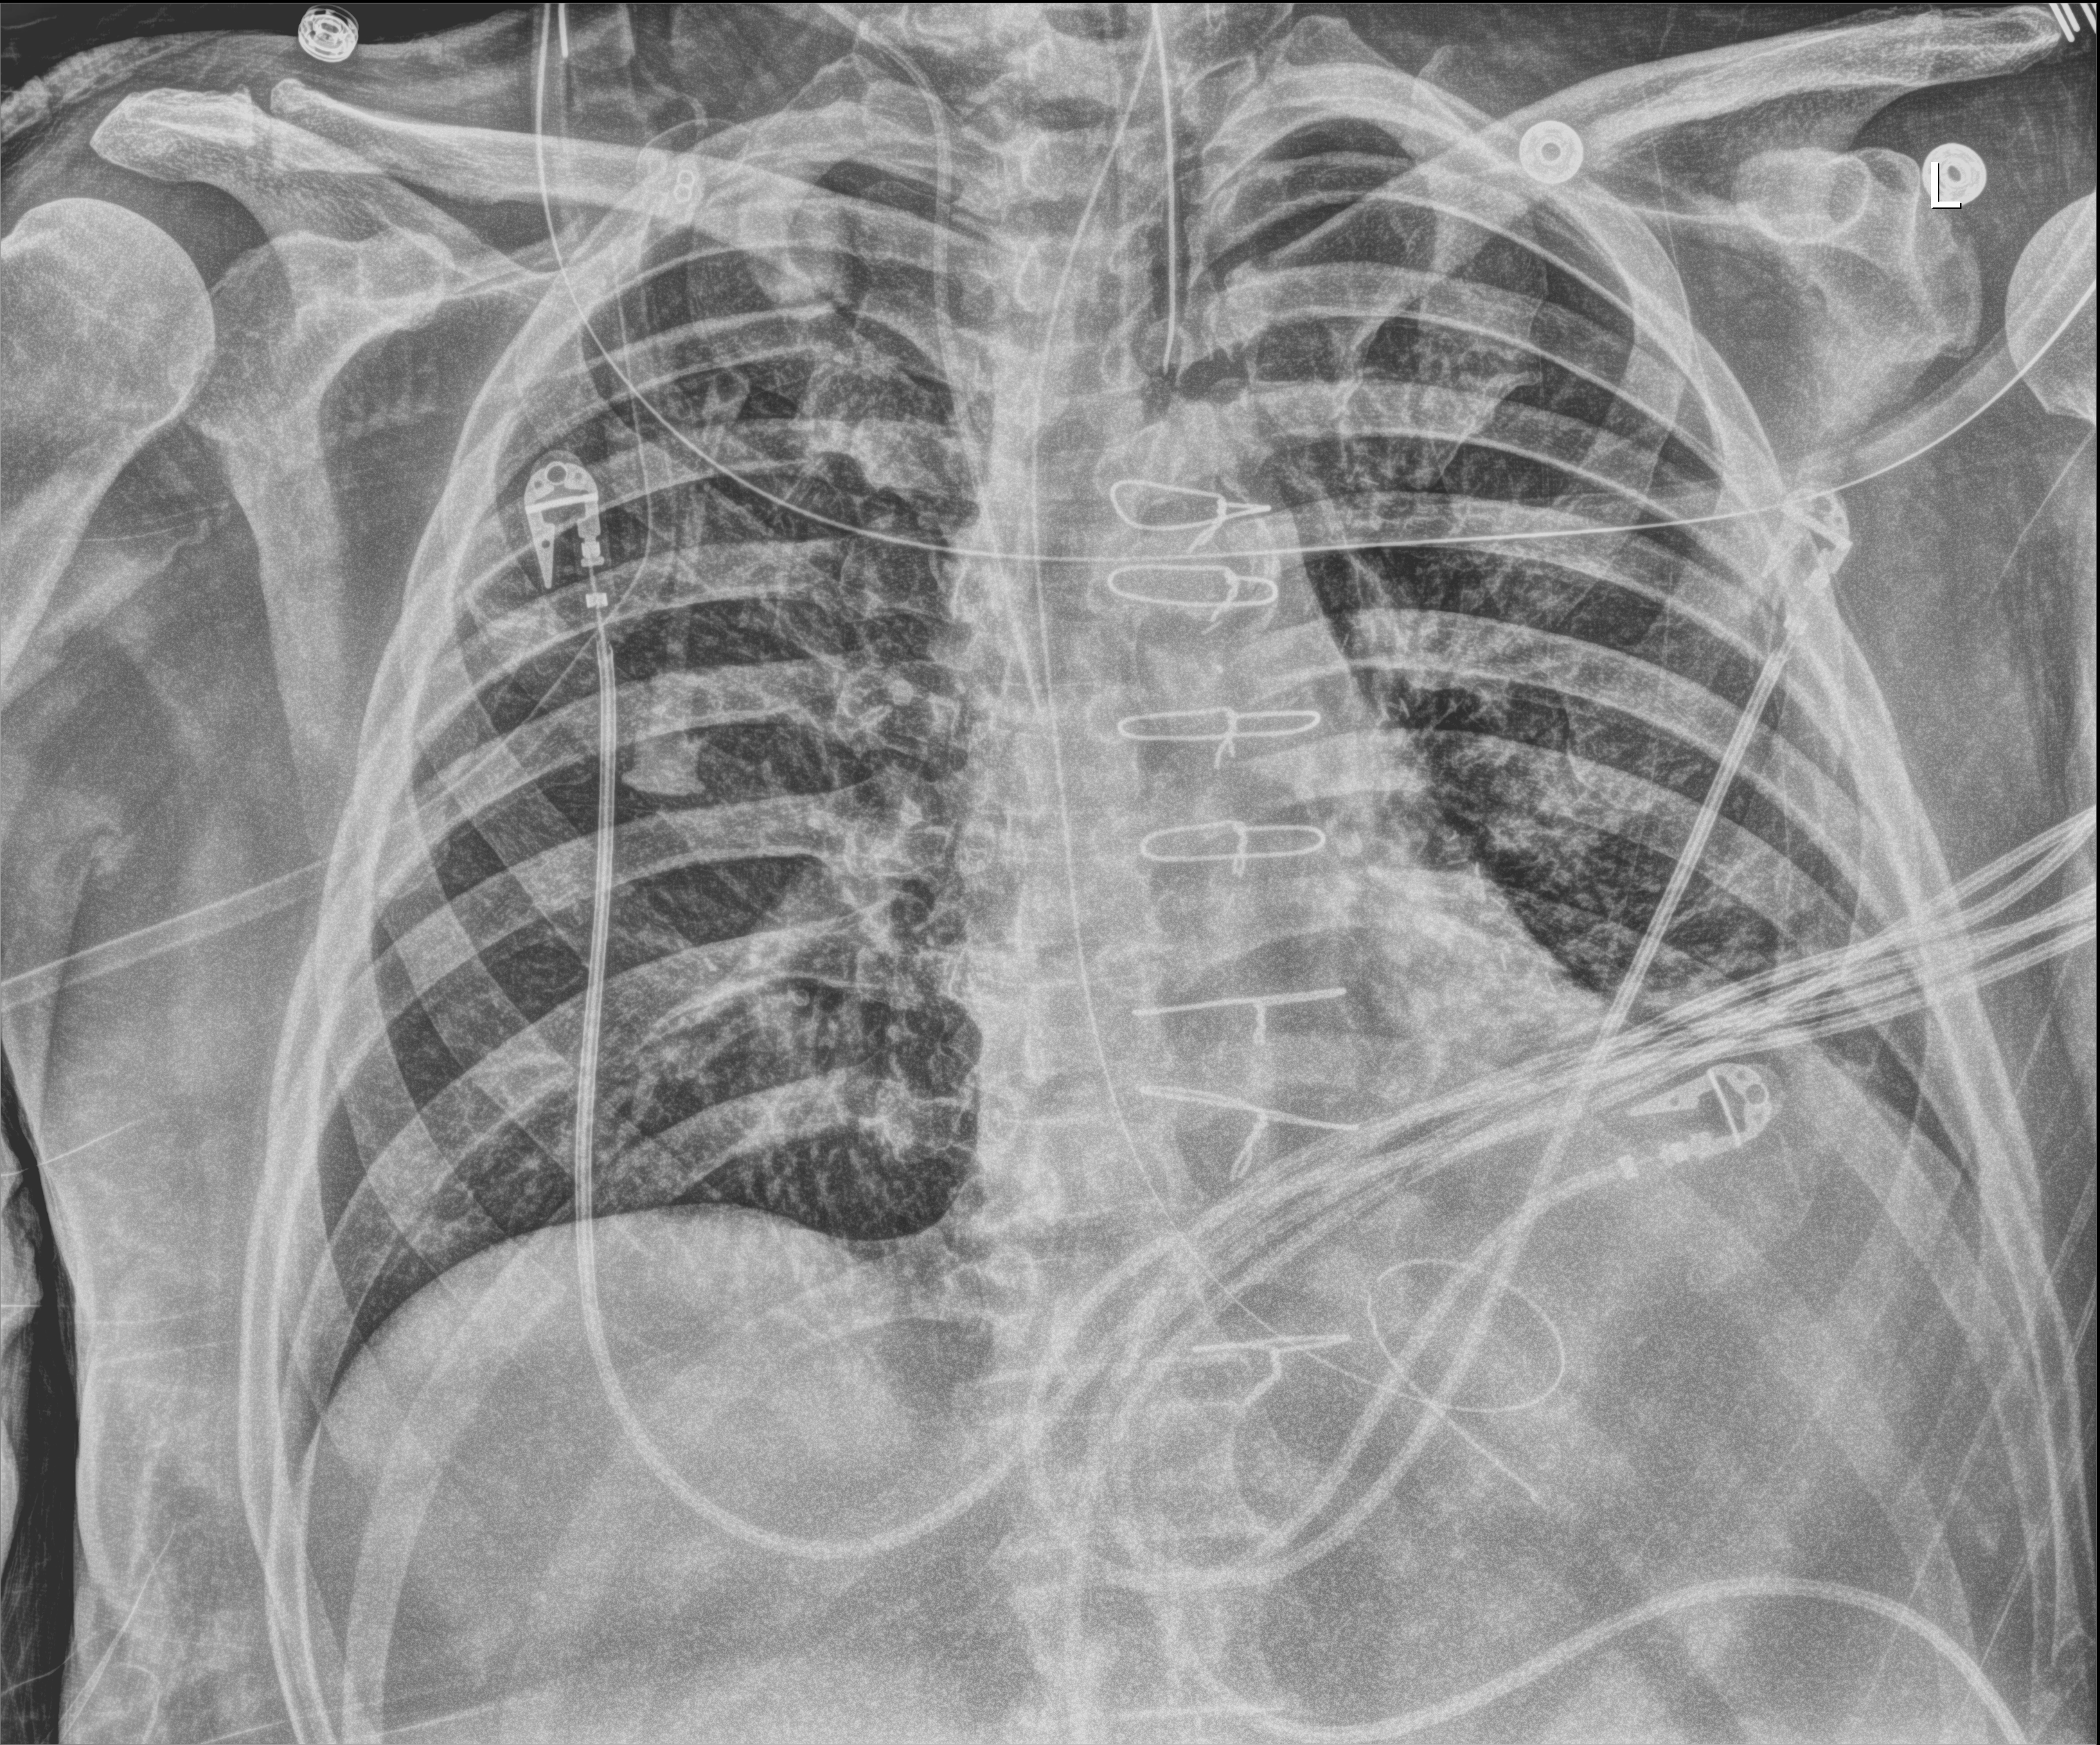
Bedside chest radiograph (digital radiography); anteroposterior (AP) projection. Male patient hospitalised with COVID-19, age 60–74 years.
Admission-level facts for this patient (not findings on this image; timing relative to this image not recorded): diabetes (admission record): yes.